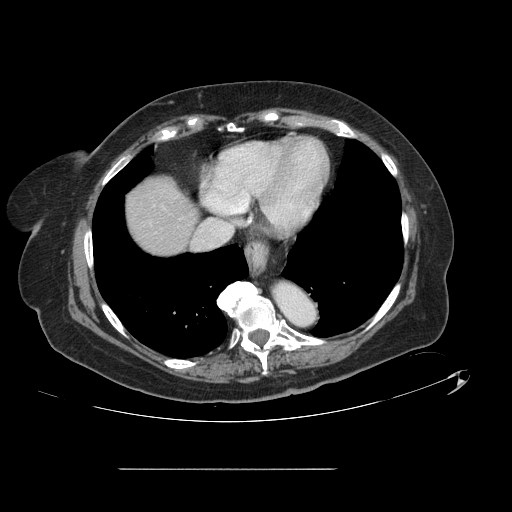
Contrast-enhanced abdominal CT, one axial slice; position 125 of 148 along the scan axis; intravenous contrast given; soft-tissue window (W 400 / L 40 HU); 2.5 mm slice thickness; 512 × 512 image matrix. Female patient, age 75 years. From the clinical record (not read from this slice): diagnosis: colorectal cancer liver metastases, imaged before liver resection; multiple liver metastases: no; largest metastasis: 2.4 cm.
Annotated regions visible in this slice (expert manual segmentation):
- liver: box from (x=127, y=178) to (x=197, y=255) px
- planned liver remnant (the part of the liver to remain after resection): (x=127, y=178)–(x=197, y=255)